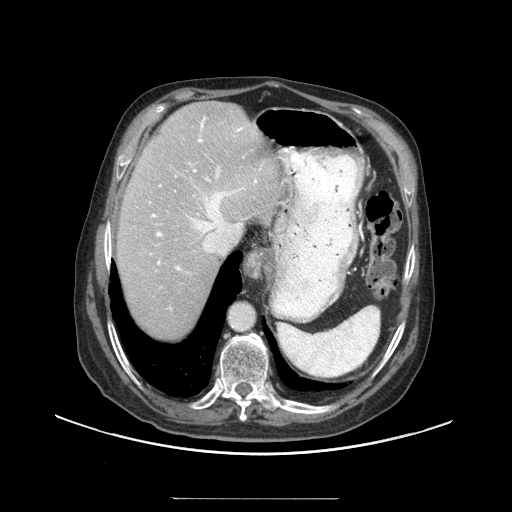
Contrast-enhanced abdominal CT (liver protocol), one axial slice. Position 77 of 97 along the scan axis. Reconstruction kernel STANDARD. Soft-tissue window (W 400 / L 40 HU). 2.5 mm slice thickness. 512 × 512 image matrix. From the clinical record (not read from this slice): diagnosis: hepatocellular carcinoma (patient treated with transarterial chemoembolisation; whether this scan precedes or follows treatment is not stated here); TNM stage (as recorded): Stage-IIIC; Child-Pugh class: A; tumour differentiation: well differentiated; tumour nodularity: uninodular.
Structures marked on this image (semi-automatically segmented with operator editing):
- abdominal aorta: bounding box [x1, y1, x2, y2] px = [230, 302, 256, 330]
- liver parenchyma outside the tumour (the mass and vessels are separate outlines, so this box may not span the whole liver): [116, 102, 283, 338]
- liver vessels: [151, 117, 261, 310]